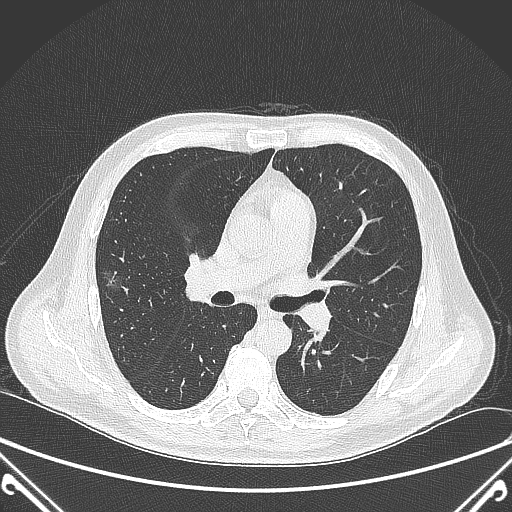
Chest CT, one axial slice. Position 217 of 360 along the scan axis. 120 kVp. Lung window (W 1500 / L -600 HU). 1 mm slice thickness. 512 × 512 image matrix, field of view 380 × 380 mm. Male patient, age 64 years. From the clinical record (not read from this slice): clinical TNM (as recorded): T1c N0 M0.
Structures marked on this image (bounding box drawn by a radiologist):
- lung tumour (recorded histology: adenocarcinoma): bounding box <98,265,131,299> (left, top, right, bottom; pixels)